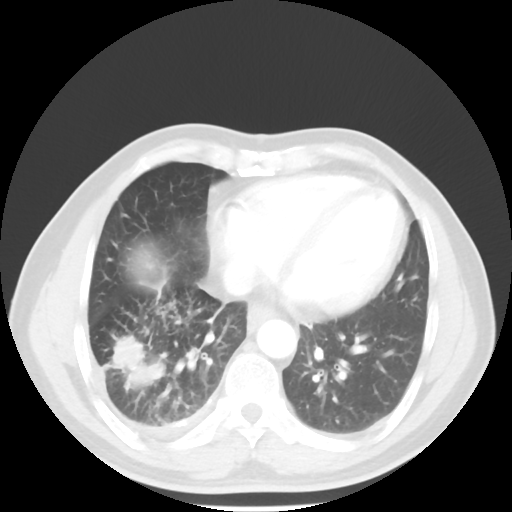
Chest CT, one axial slice; slice 20 of 56 in the series (ordered by position); 120 kVp; lung window (W 1500 / L -600 HU); 5 mm slice thickness; 512 × 512 image matrix. Patient: male, 56 years. Case-level facts recorded for this patient, not image findings: clinical TNM (as recorded): T2 N3 M1.
Annotated regions visible in this slice (bounding box drawn by a radiologist):
- lung tumour (recorded histology: adenocarcinoma): bounding box (x1, y1, x2, y2) in pixels: (112, 332, 172, 400)